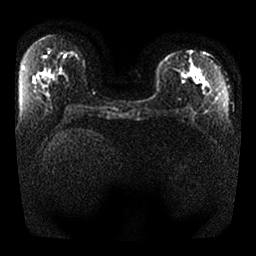
Breast MRI, one axial slice. Slice 13 of 25 in the series (ordered by position). Diffusion-weighted series; image 2 of 4 stored at this slice position (different b-values; order by instance number). 1.5 T. 256 × 256 image matrix. Female patient.
Outlined on this slice (outlined manually by an expert reader):
- tumour on diffusion-weighted imaging: bounding box <180,69,200,84> (left, top, right, bottom; pixels)